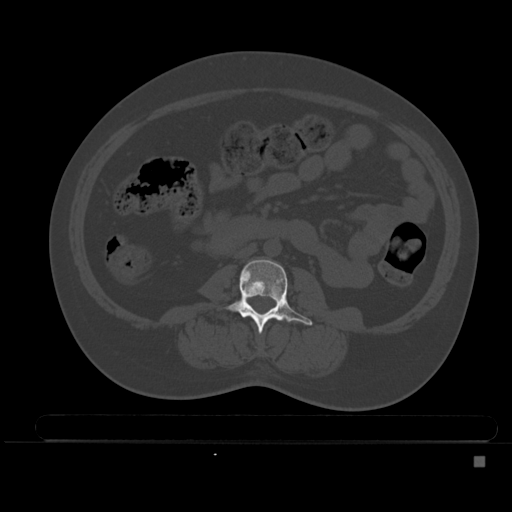
CT including the spine, one axial slice; bone window (W 1800 / L 400 HU); 1.5 mm slice thickness; 512 × 512 image matrix, field of view 404 × 404 mm. Female patient, age 33 years. From the clinical record (not read from this slice): primary cancer: breast; vertebrae with lytic lesions (as recorded): T1.
Structures marked on this image (semi-automatically segmented with operator editing):
- L3 vertebra: box from (x=220, y=259) to (x=313, y=333) px